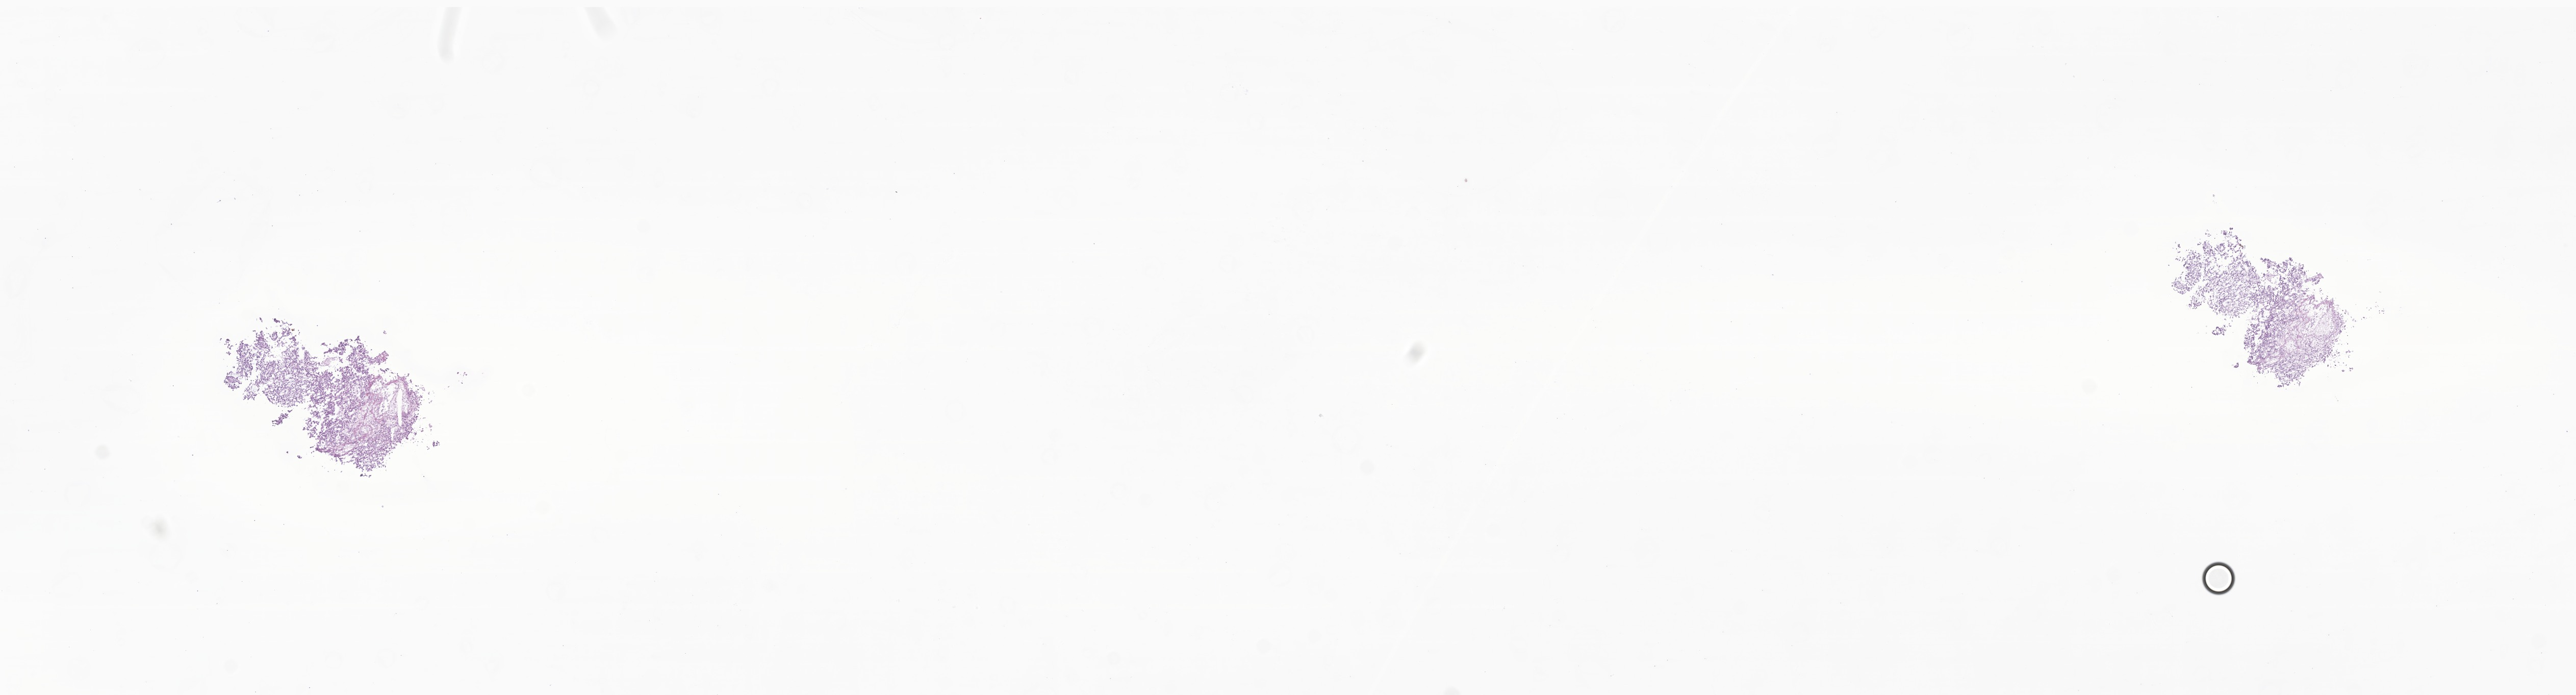
Digitized hematoxylin and eosin (H&E)-stained section of tumor tissue from the spinal cord, shown as a low-resolution overview of the whole scanned area (about 21.3 x 5.7 mm), cryosection (OCT / tissue freezing medium). Male patient, age 75 months (6 years 3 months).
Diagnosis (ICD-O-3 morphology term): Myxopapillary ependymoma.